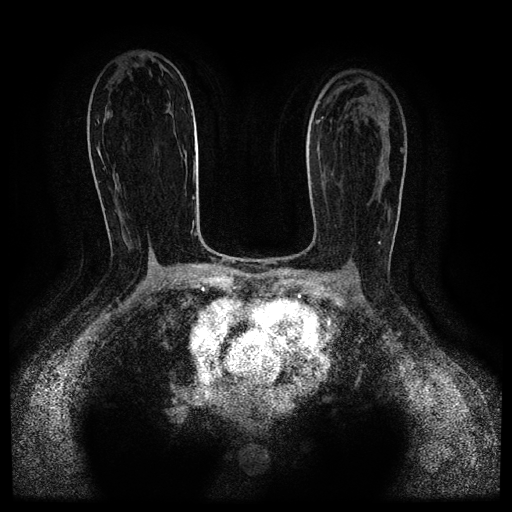
Breast MRI (dynamic contrast-enhanced, multi-phase), one axial slice; position 59 of 116 along the scan axis; dynamic contrast-enhanced series, time point 2 of 5 at this slice position (early post-contrast); 1.5 T; TE 2.6 ms, TR 5.3 ms; 2 mm slice thickness; 512 × 512 image matrix, field of view 350 × 350 mm. Female patient, age 52 years.
Structures marked on this image (semi-automatic segmentation, software-assisted and operator-edited):
- breast lesion (labelled 'tumour' in the annotation; benign lesions carry a separate 'benign' label): bounding box (x1, y1, x2, y2) in pixels: (380, 114, 389, 132)